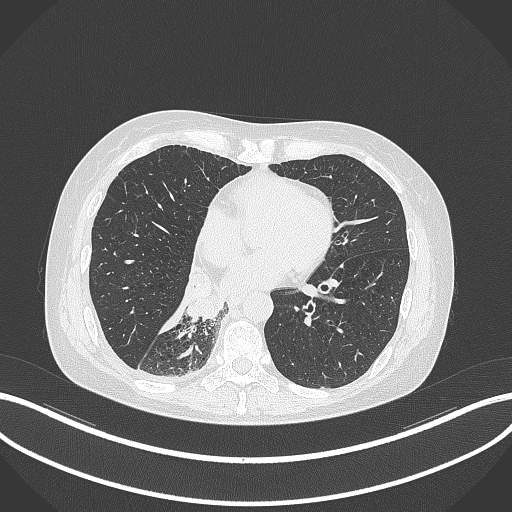
Chest CT, one axial slice. Position 120 of 329 along the scan axis. 120 kVp. Lung window (W 1500 / L -600 HU). 1 mm slice thickness. 512 × 512 image matrix, field of view 400 × 400 mm. Patient: female, 63 years. From the clinical record (not read from this slice): clinical TNM (as recorded): T1c N0 M0.
Structures marked on this image (rectangle marked by the reading radiologist):
- lung tumour (recorded histology: adenocarcinoma): bounding box <176,268,230,324> (left, top, right, bottom; pixels)